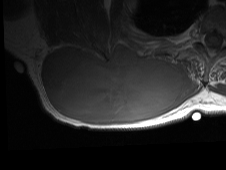
MRI of an extremity soft-tissue mass, one axial slice. Position 37 of 81 along the scan axis. MR volume resampled by the dataset authors to the PET/CT grid (not the native acquisition matrix). 226 × 170 image matrix. Male patient. Case-level facts recorded for this patient, not image findings: histological type: pleiomorphic spindle cell undifferentiated; grade: high; site of the primary tumour: right parascapusular.
Structures marked on this image (expert contour drawn on MRI and transferred to this co-registered scan by the dataset authors):
- gross tumour volume including surrounding oedema: bounding box [x1, y1, x2, y2] px = [41, 45, 198, 126]
- gross tumour volume (mass): [41, 45, 184, 123]